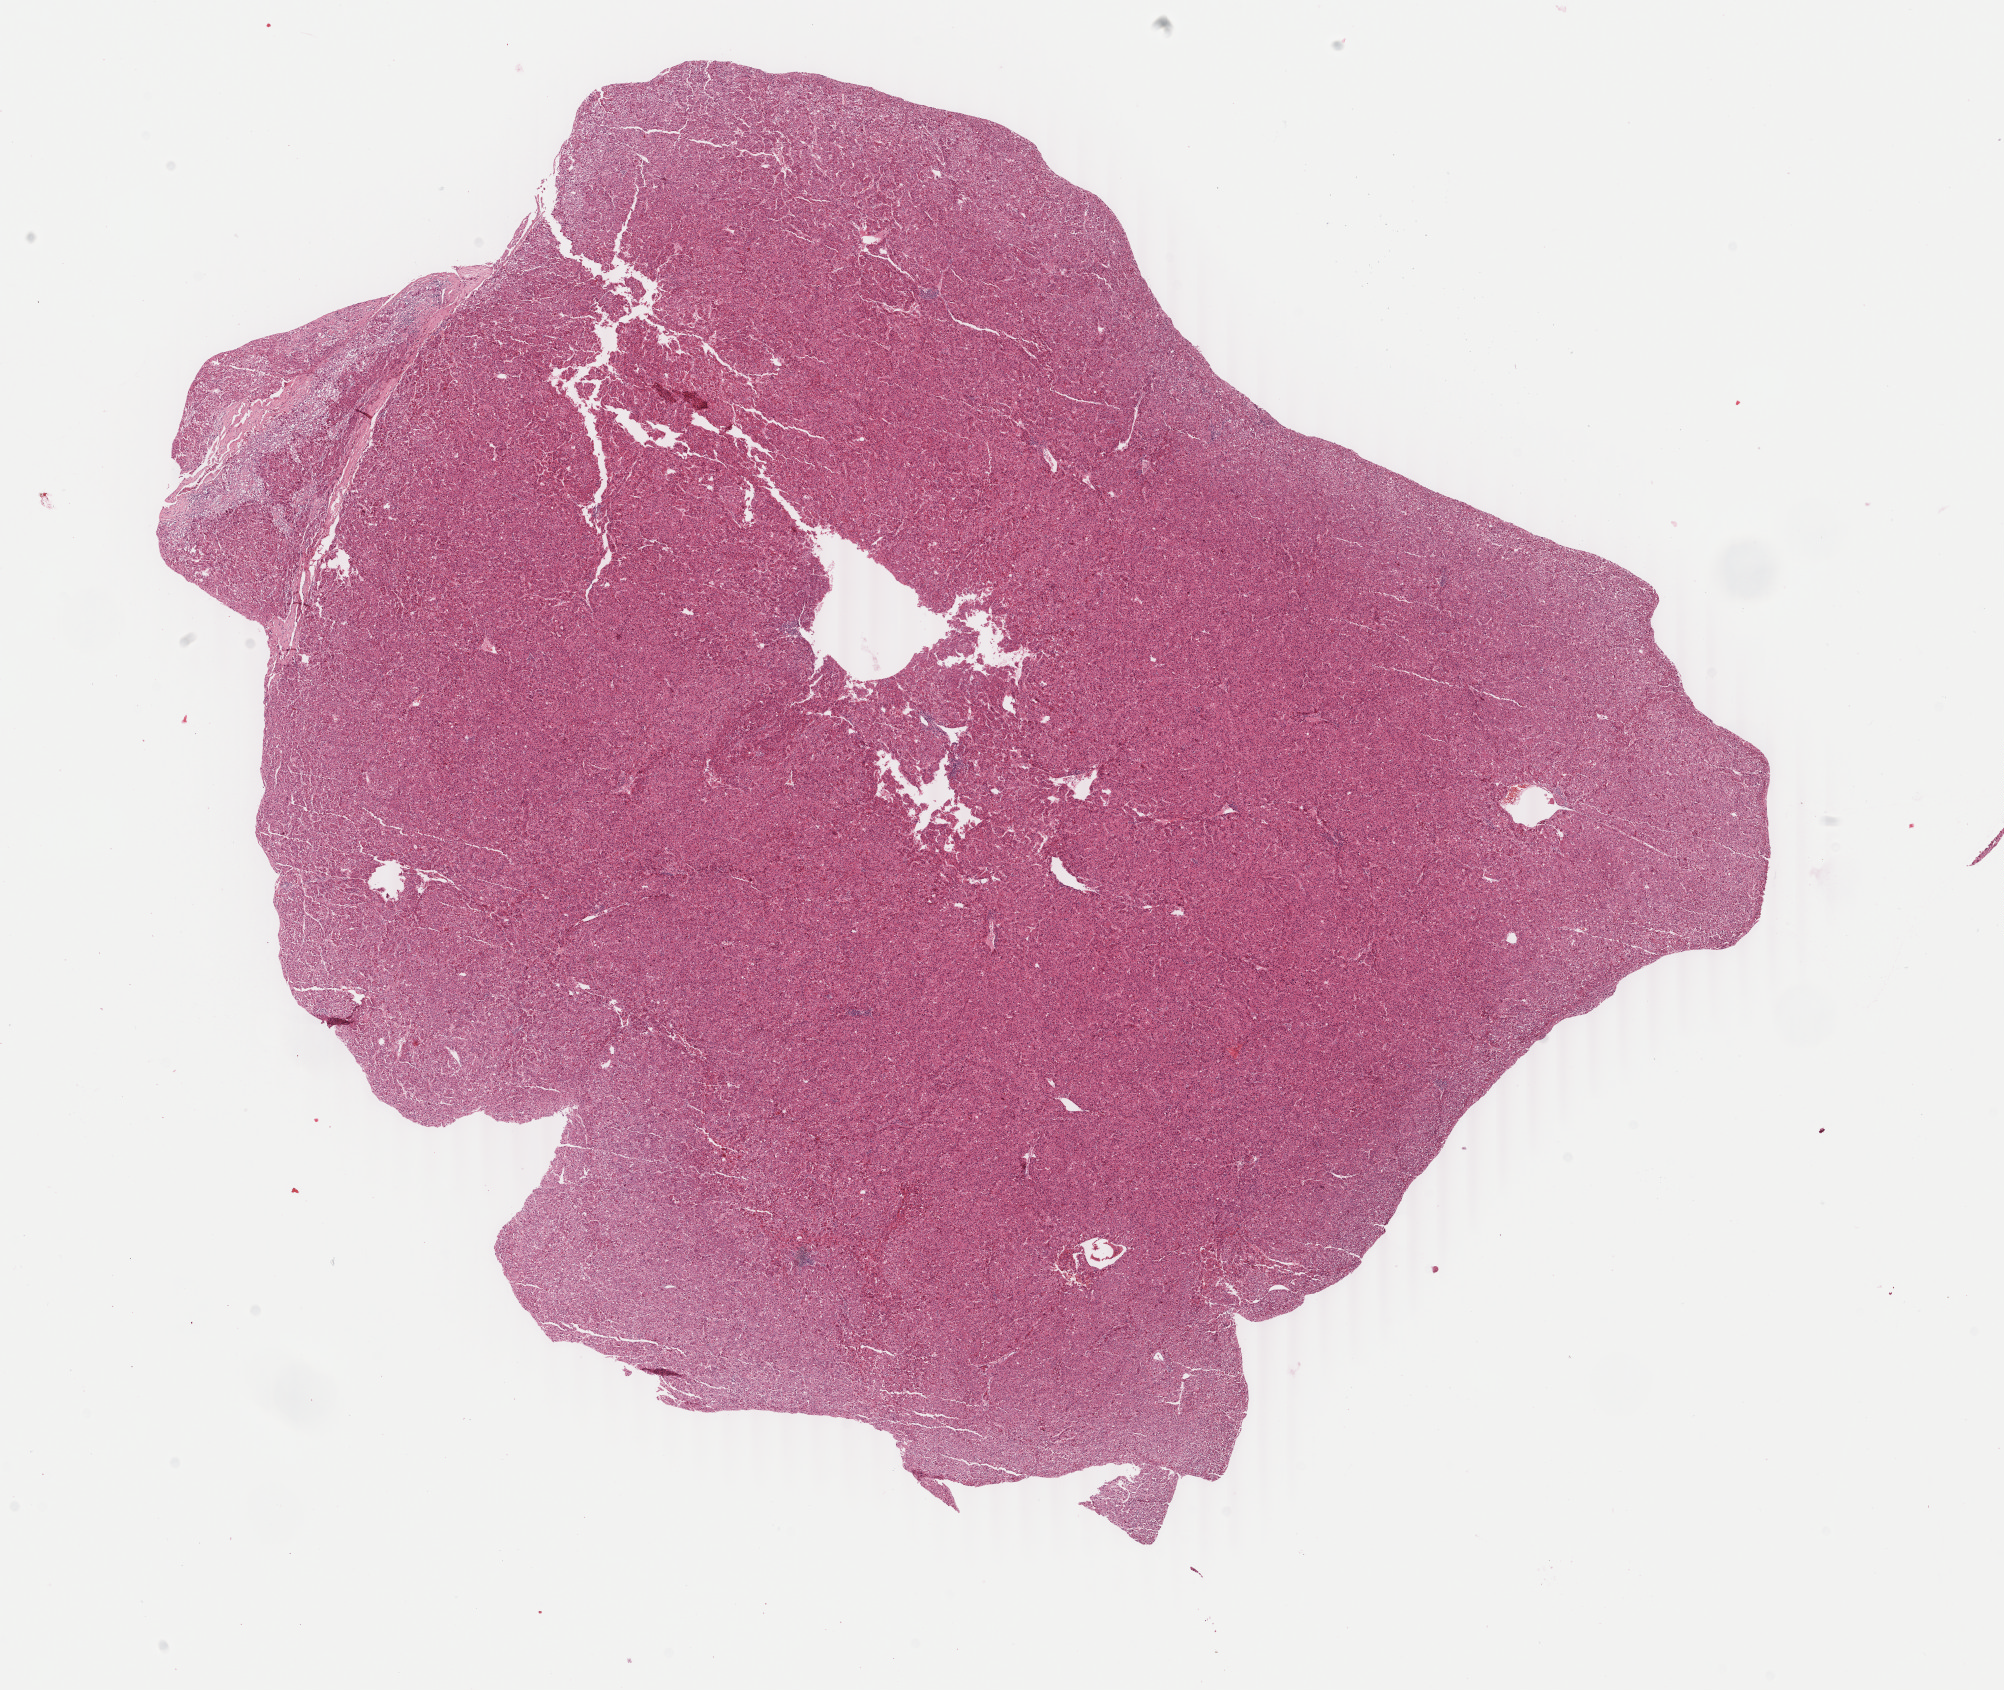
Hematoxylin and eosin (H&E) stained whole-slide image, low-resolution overview of the scanned area, about 15.9 x 13.4 mm; FFPE section; liver, primary tumour sample. Patient: male, age at initial diagnosis 57 years. Histologic grade: G2 (moderately differentiated).
Diagnosis: Hepatocellular carcinoma, NOS. AJCC pathologic stage: II (7th edition). TNM: T2 N0 M0.